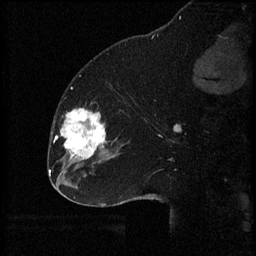
Breast MRI (dynamic contrast-enhanced), one sagittal slice; slice 23 of 60 in the series (ordered by position); 3 images stored at this slice position (order not interpretable as contrast timing); 1.5 T; TE 4.2 ms, TR 8.2 ms; 2 mm slice thickness; 256 × 256 image matrix, field of view 180 × 180 mm. Female patient, age 32 years.
Structures marked on this image (semi-automatic segmentation, software-assisted and operator-edited):
- analysis volume of interest (the breast-tissue region the enhancement analysis was run in; not a lesion): bounding box [x1, y1, x2, y2] px = [60, 108, 111, 165]
- tumour enhancement mask (voxels above the 70 % enhancement threshold inside the analysis volume of interest): [61, 108, 106, 161]